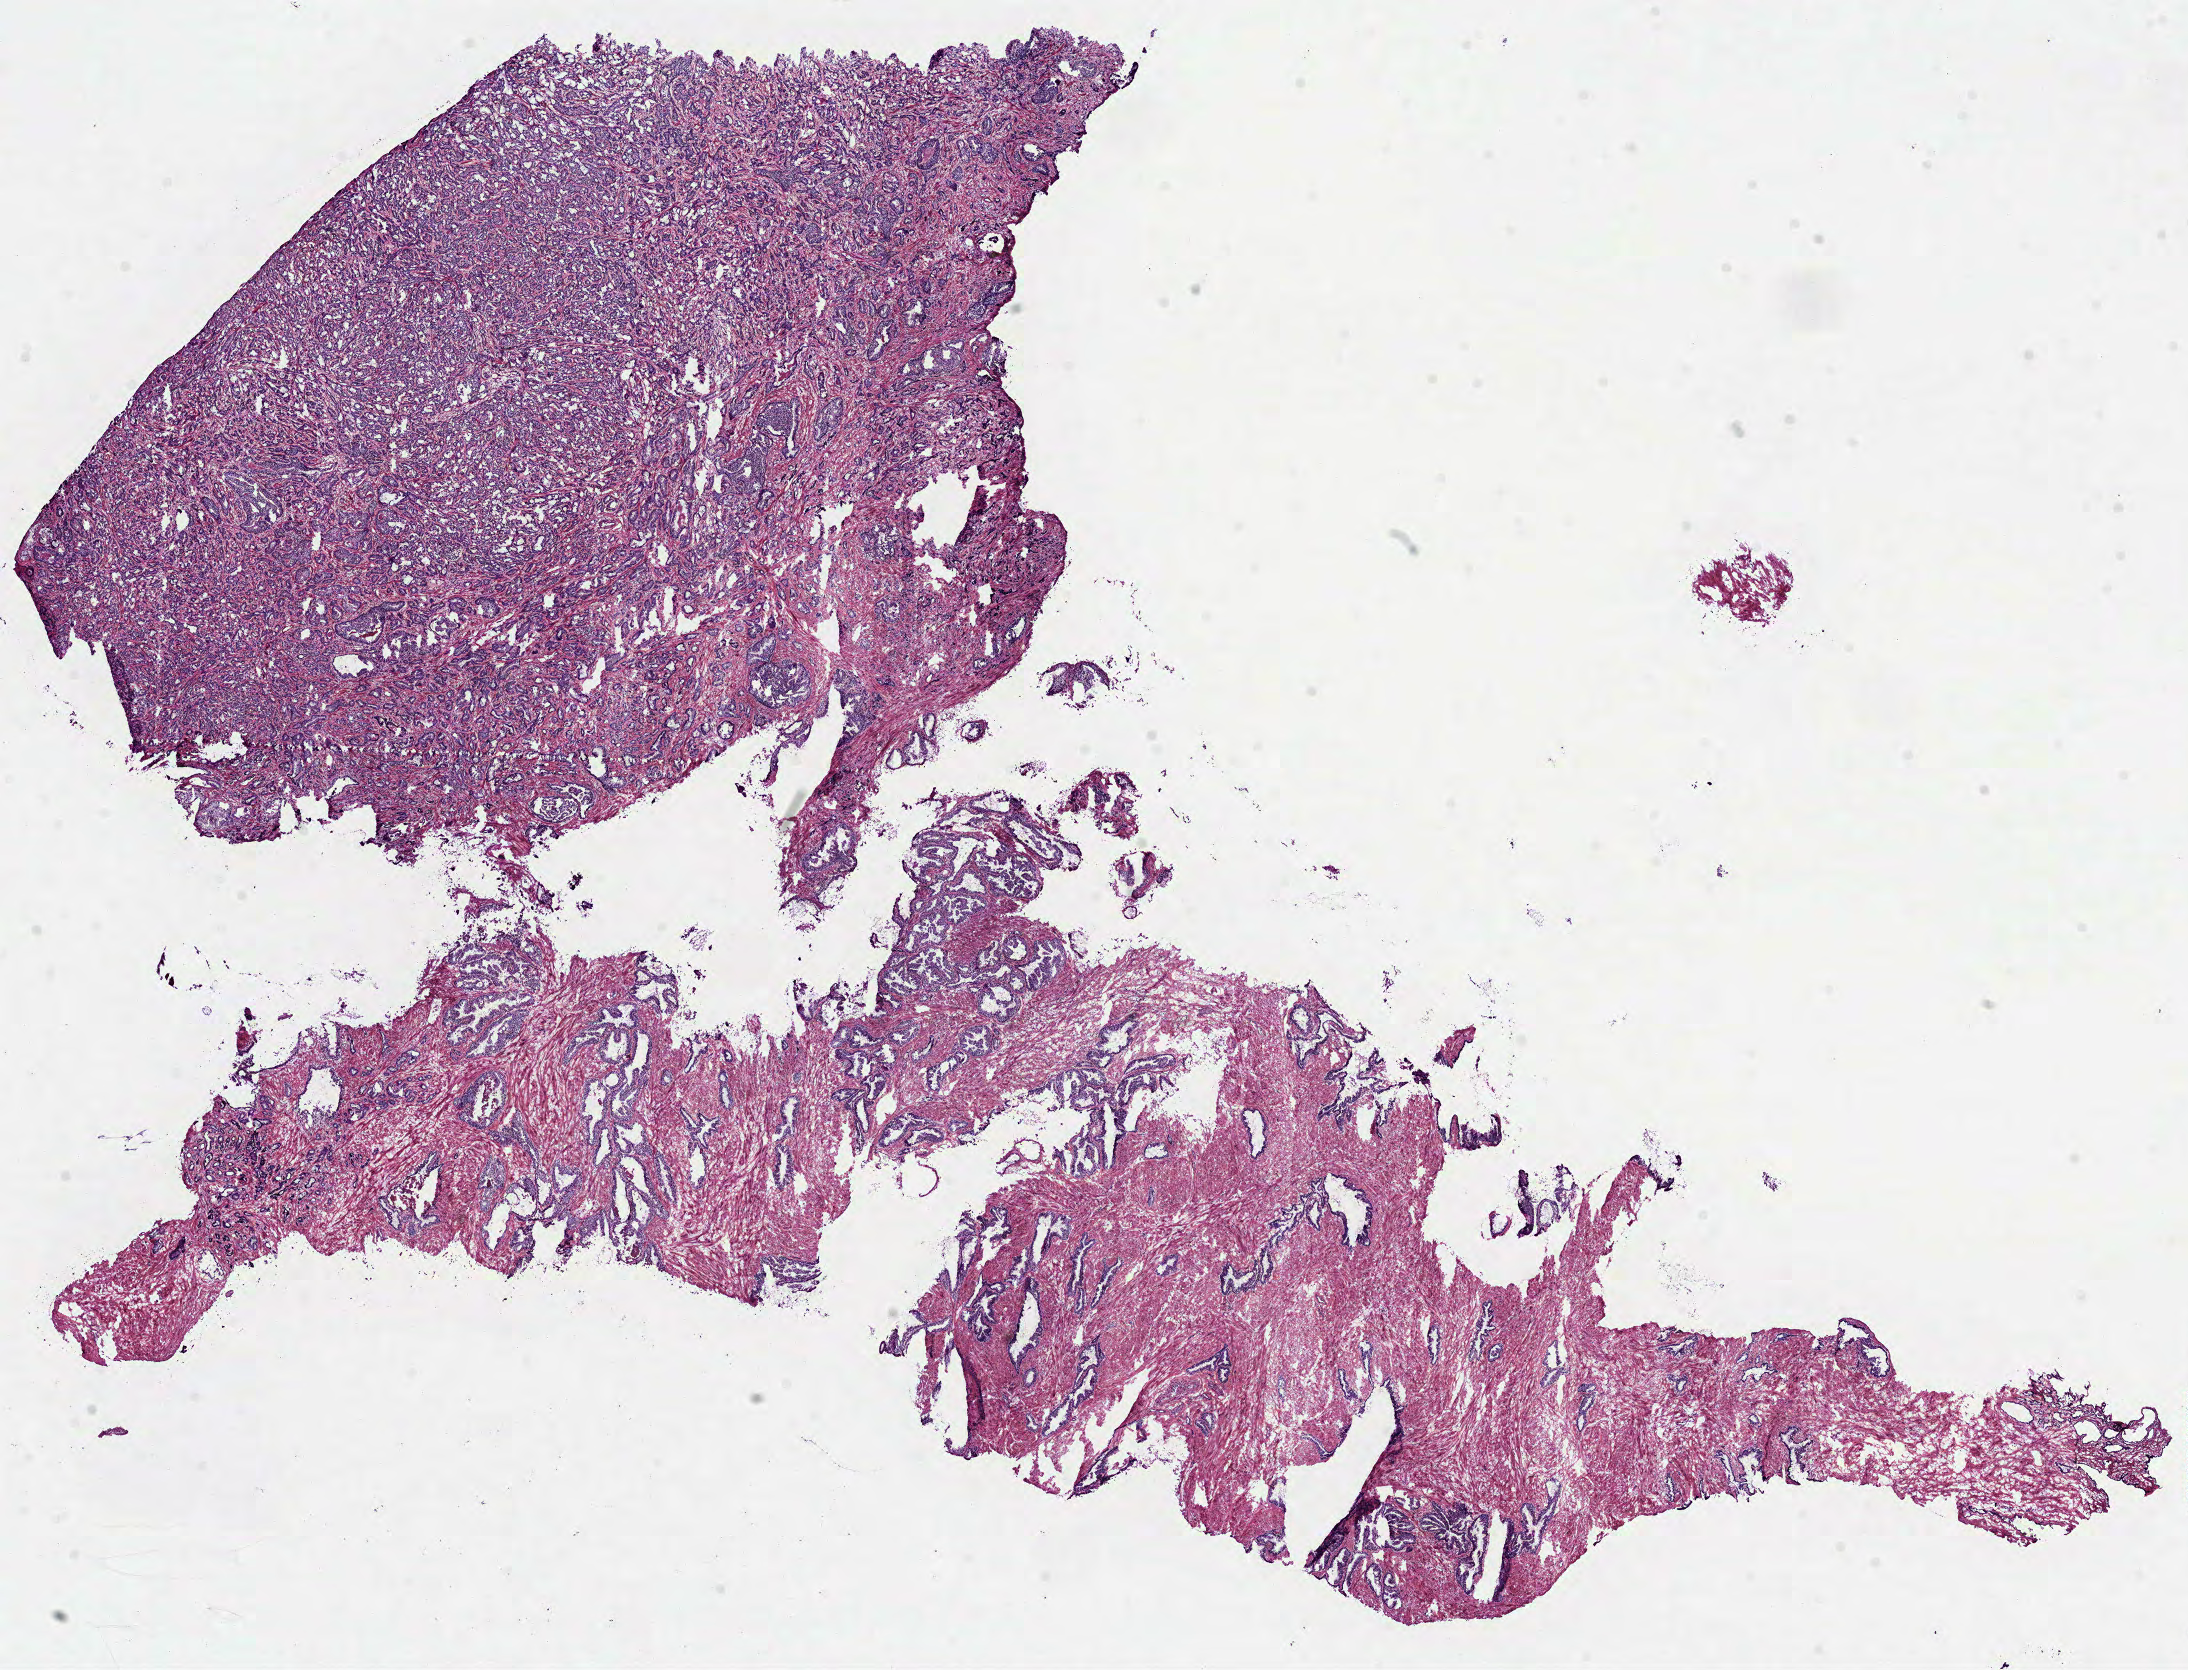
Digitized Hematoxylin and eosin (H&E) stained tissue section (whole slide) — low-resolution overview of the scanned area, about 17.6 x 13.5 mm (slide scanned at 40x). Frozen section from the top of the tissue portion. Prostate, primary tumour sample. Male, age 61 years at initial diagnosis. Gleason score: 7 (3+4). Composition of this section per pathologist review: tumour cells 65%, tumour nuclei 65%, normal cells 20%, stromal cells 15%, necrosis 0%. Inflammatory infiltration, as recorded: lymphocyte infiltration 4%, monocyte infiltration 0%, neutrophil infiltration 0%.
- lymph nodes positive (case pathology): 0 of 17 examined
- histologic diagnosis: Acinar cell carcinoma (prostate gland)